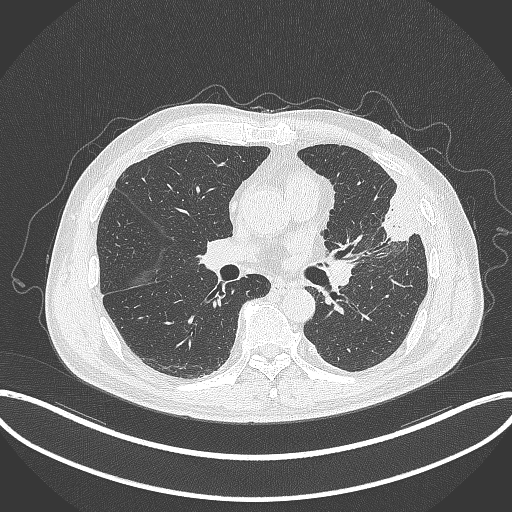
Chest CT, one axial slice; position 175 of 382 along the scan axis; lung window (W 1500 / L -600 HU); 512 × 512 image matrix, field of view 415 × 415 mm. Patient: male, 64 years. Case-level facts recorded for this patient, not image findings: clinical TNM (as recorded): T4 N1 M0; histopathological grade: G3.
Structures marked on this image (bounding box drawn by a radiologist):
- lung tumour (recorded histology: adenocarcinoma): box from (x=376, y=182) to (x=421, y=244) px